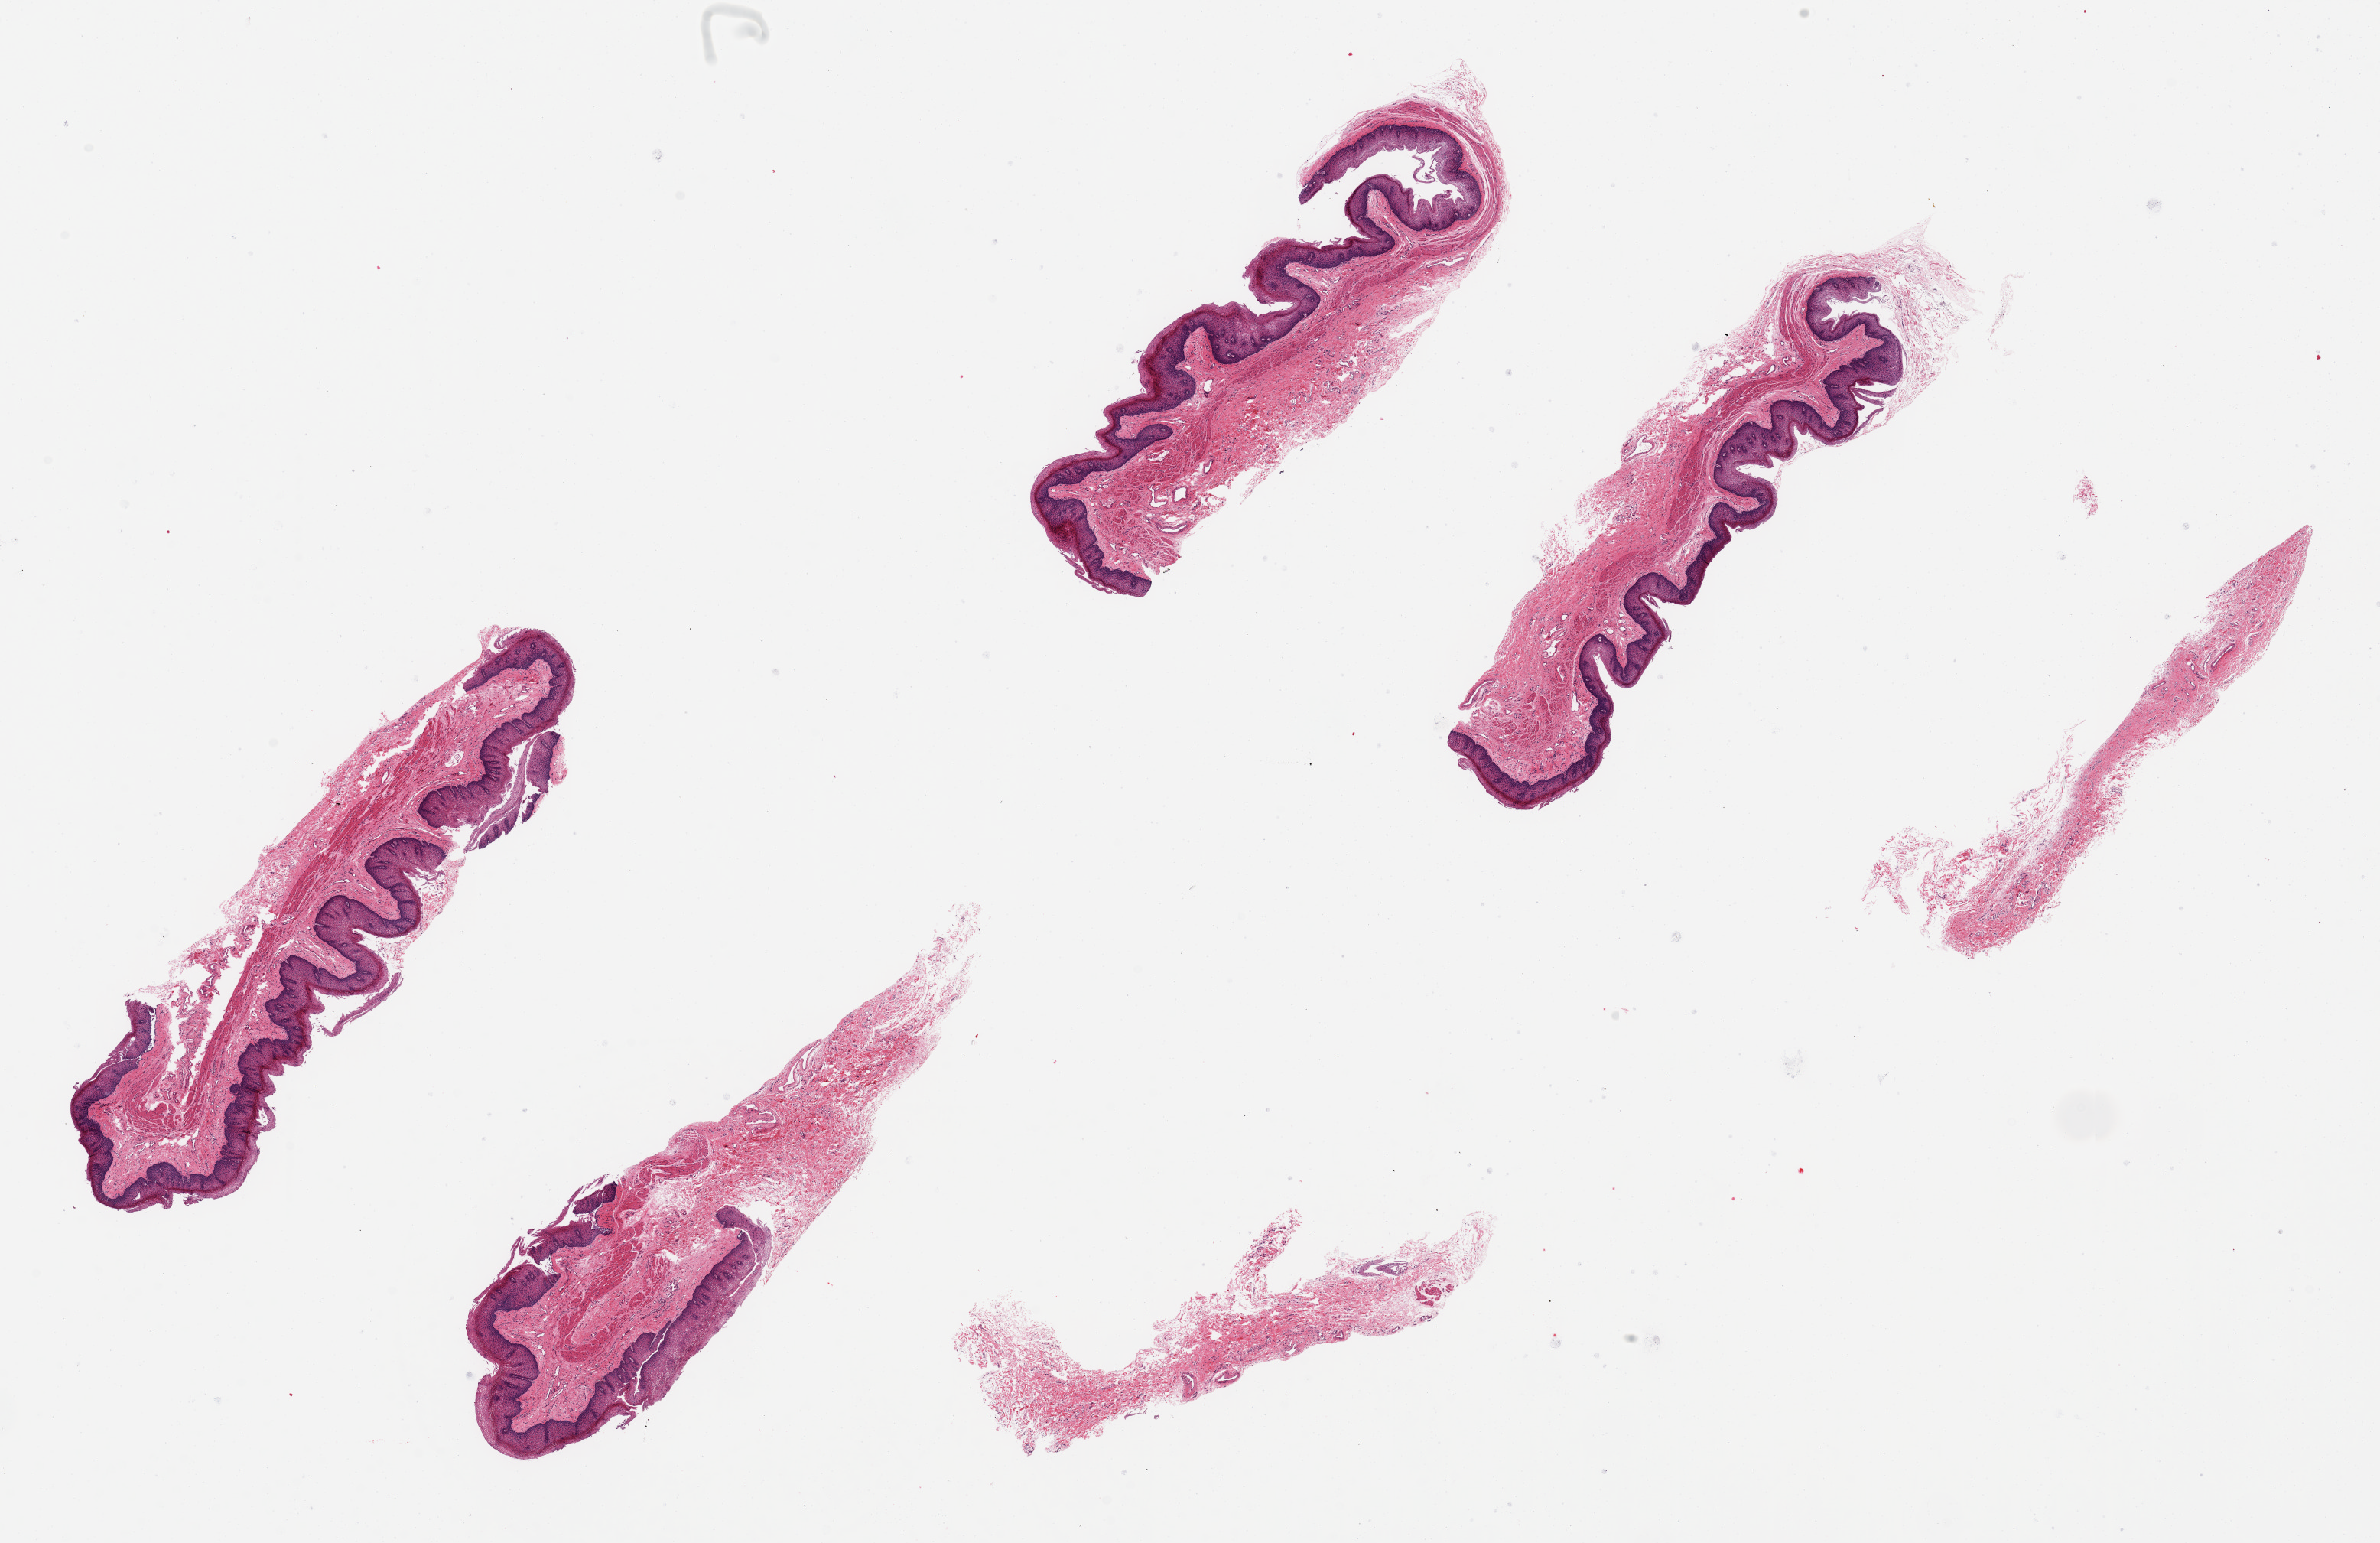
Haematoxylin and eosin whole-slide image — shown as a low-resolution overview of the whole scanned area (about 24.6 x 16.0 mm). PAXgene-fixed paraffin-embedded (PFPE) section. Section of esophageal mucous membrane (target tissue). Donor tissue sample.
Review note (as recorded): 6 pieces, 4 with mucosa, 2 without, mucosa up to 0.4mm; up to 7.5x2mm.